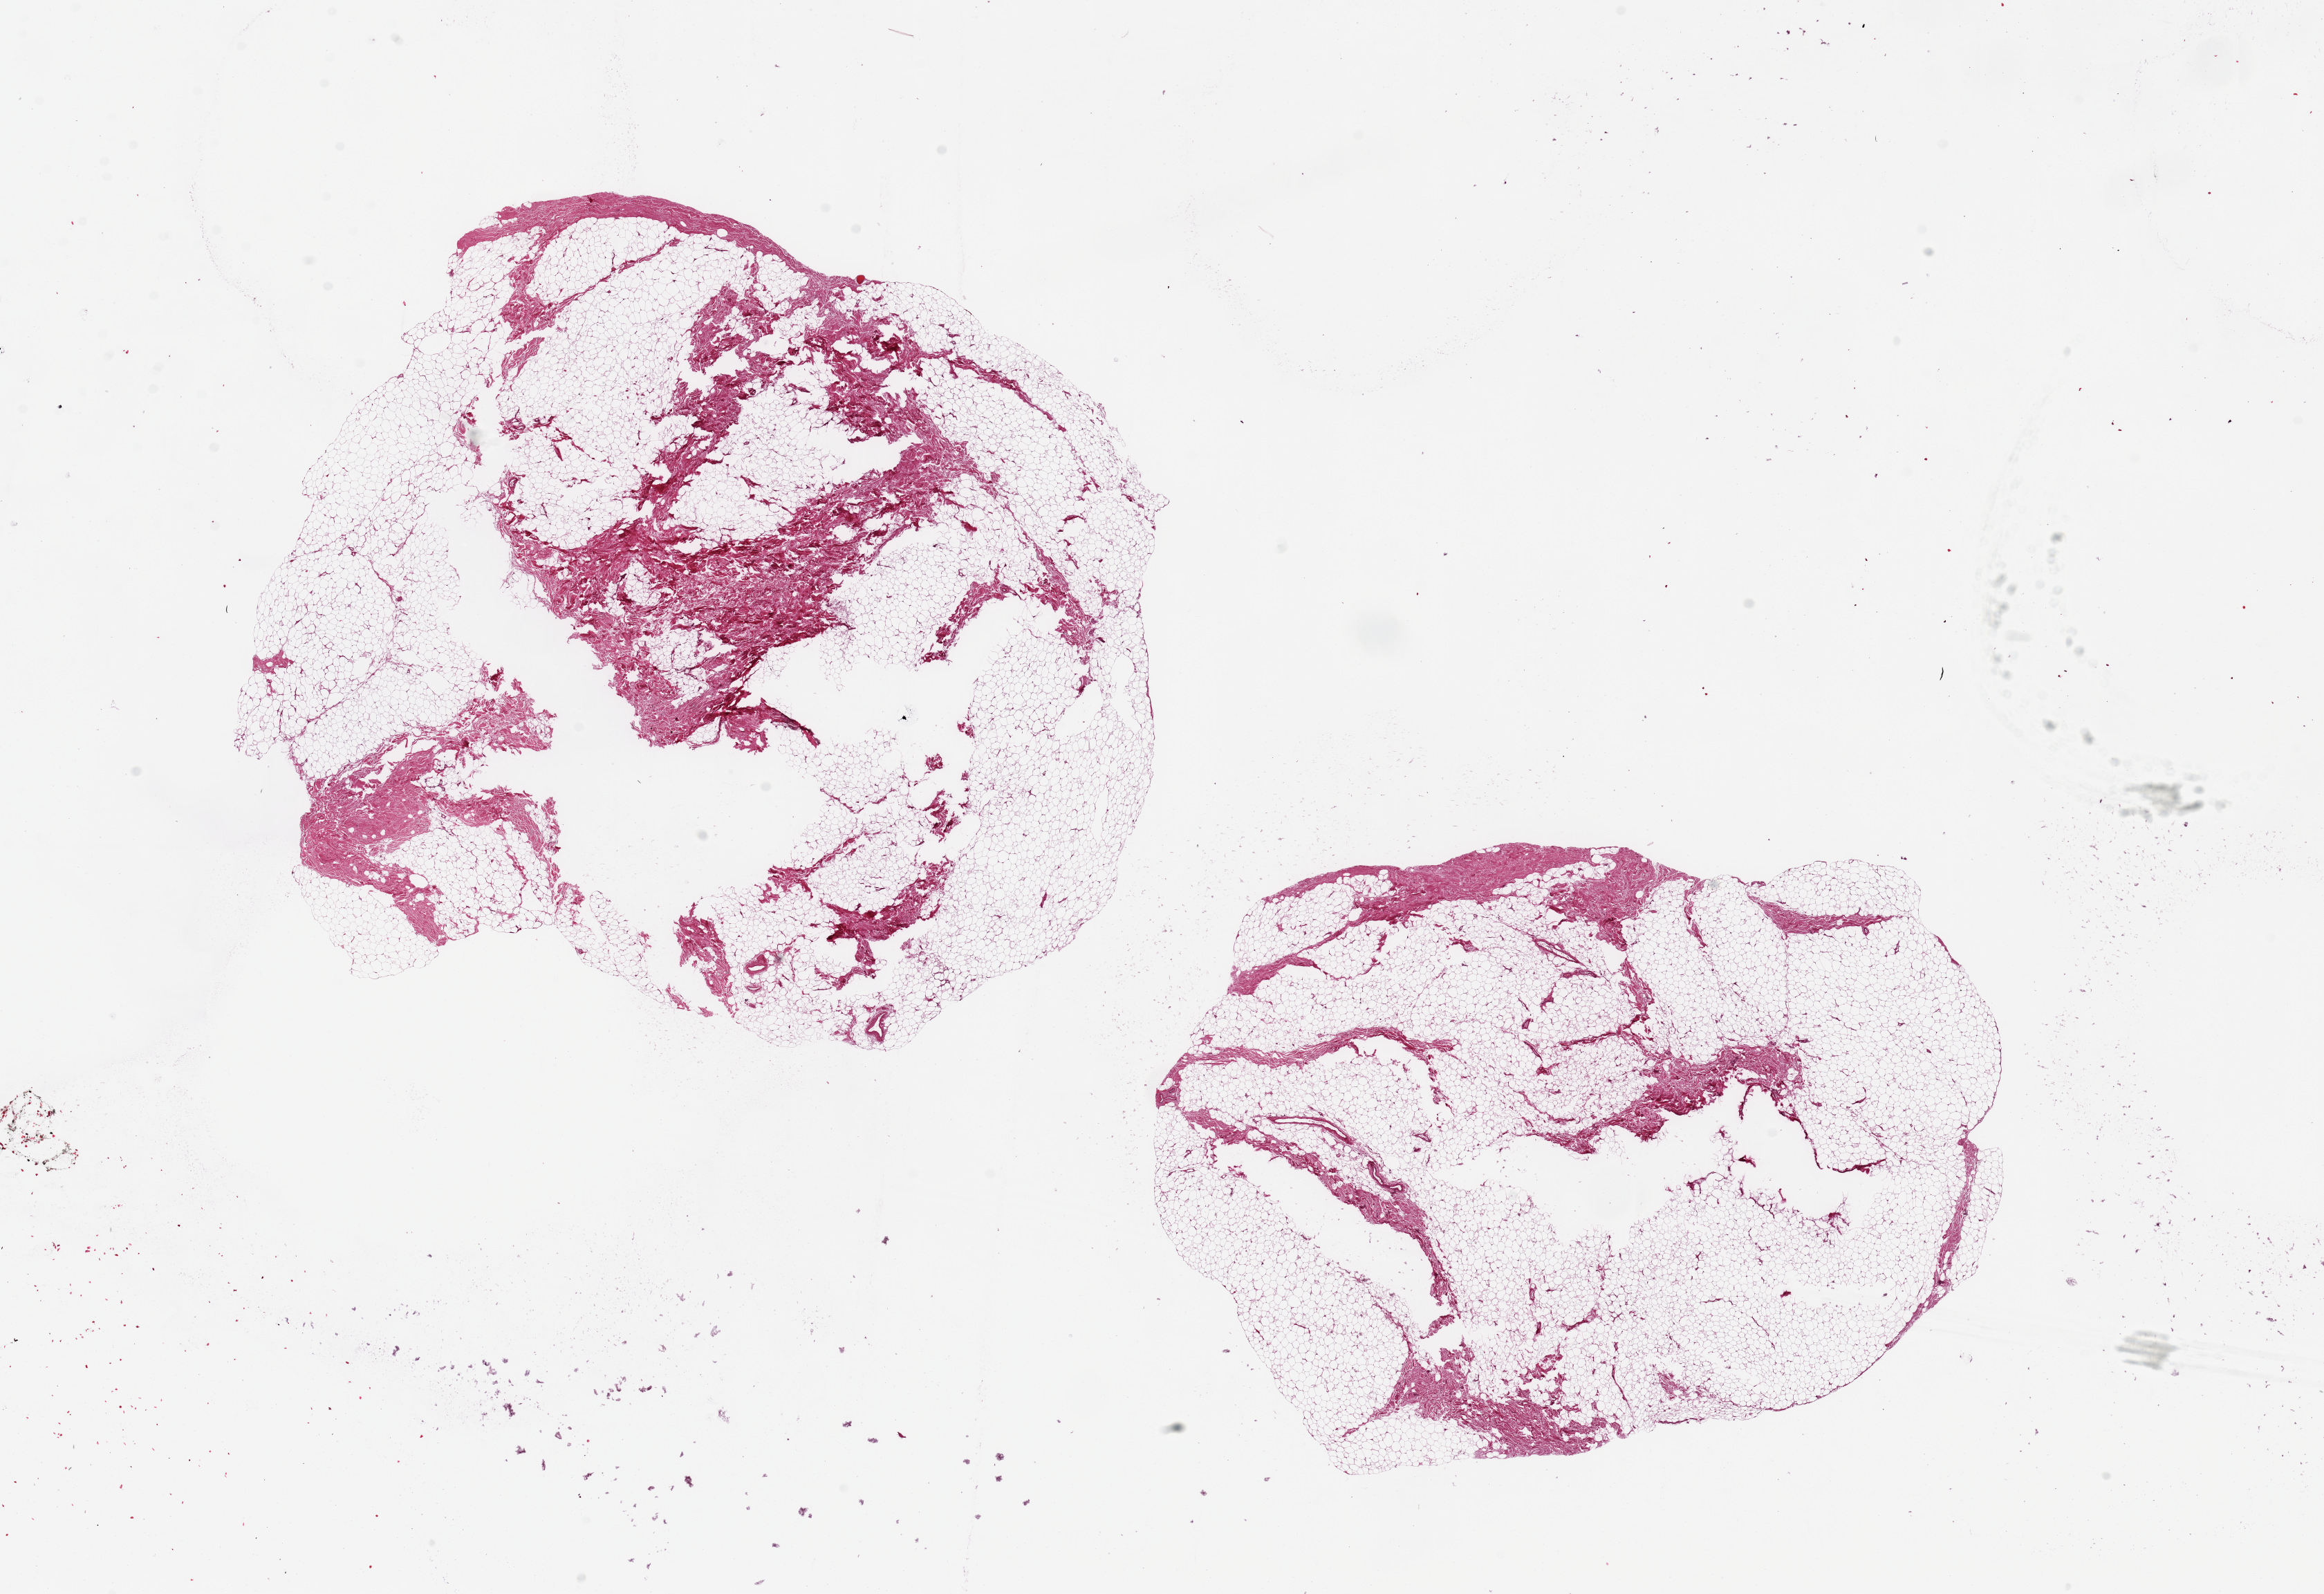
Hematoxylin and eosin (H&E) whole-slide image, low-resolution overview of the scanned area, about 26.6 x 18.2 mm (from a 20x scan). PAXgene-fixed, paraffin-embedded tissue. Sampled site (target tissue): breast. Donor tissue sample. Donor: male.
Reviewer comment on this tissue sample: 2 pieces ~9x8mm, all fibroadipose tissue, no ductal elements noted.